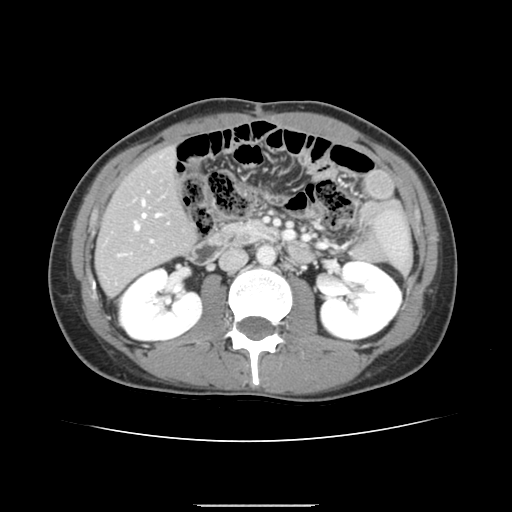
Contrast-enhanced abdominal CT, one axial slice; 120 kVp; intravenous contrast given; soft-tissue window (W 400 / L 40 HU); 2.5 mm slice thickness; 512 × 512 image matrix. Female patient, age 32 years. Case-level facts recorded for this patient, not image findings: diagnosis: colorectal cancer liver metastases, imaged before liver resection; multiple liver metastases: yes; largest metastasis: 0.7 cm; disease in both lobes: no.
Annotated regions visible in this slice (expert manual segmentation):
- hepatic veins: bounding box <135,201,161,230> (left, top, right, bottom; pixels)
- liver: <97,149,194,296>
- planned liver remnant (the part of the liver to remain after resection): <97,149,194,293>
- portal vein (with intrahepatic branches): <120,191,153,256>